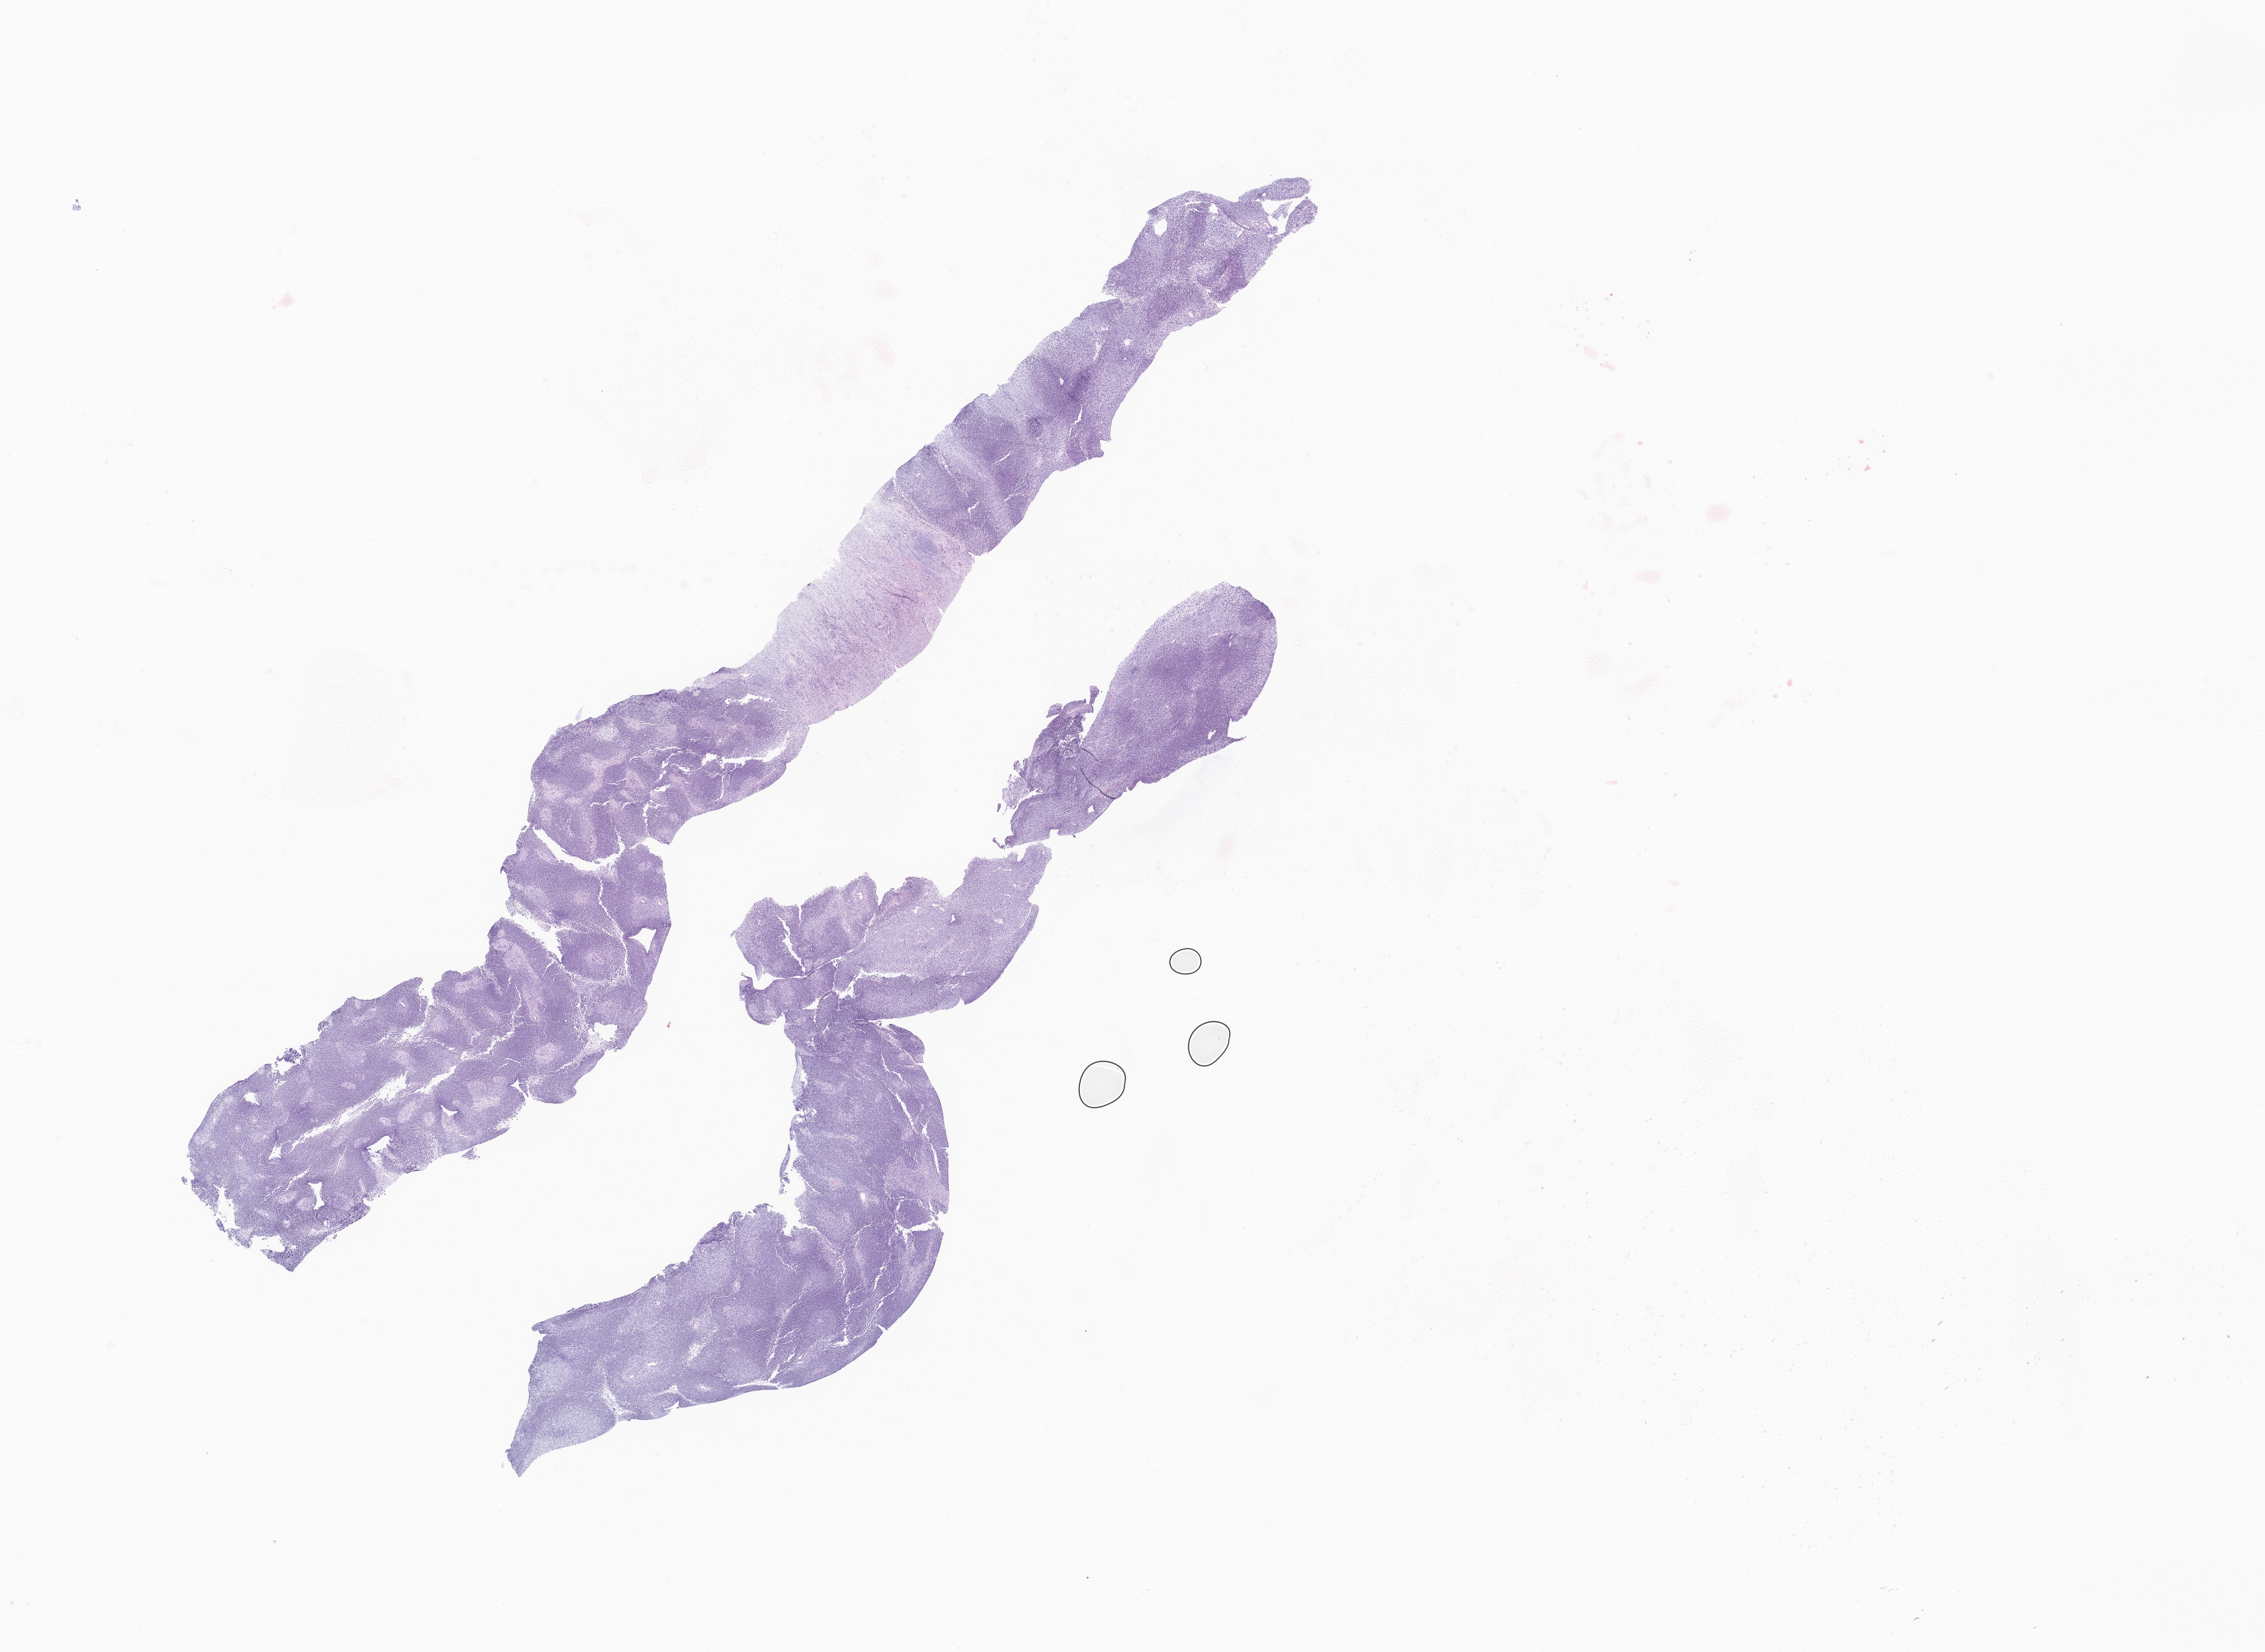
Haematoxylin and eosin whole-slide image of tumor tissue from the abdomen — whole scanned area (about 24.2 x 17.7 mm) shown as a low-resolution overview; formalin-fixed, paraffin-embedded (FFPE) tissue. Patient male; age 63 months (5 years 3 months).
- diagnosis: Rhabdomyosarcoma, NOS